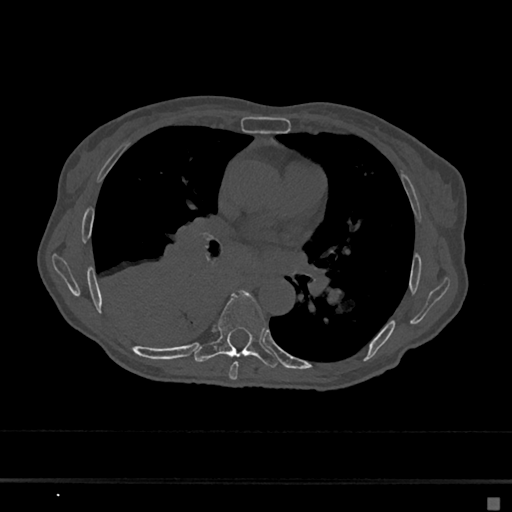
CT including the spine, one axial slice; slice 384 of 797 in the series (ordered by position); 120 kVp; bone window (W 1800 / L 400 HU); 0.5 mm slice thickness; 512 × 512 image matrix, field of view 360 × 360 mm. Patient: female, 68 years. From the clinical record (not read from this slice): primary cancer: renal.
Annotated regions visible in this slice (semi-automatically segmented with operator editing):
- T6 vertebra: bounding box <229,362,238,380> (left, top, right, bottom; pixels)
- T7 vertebra: <194,291,277,368>